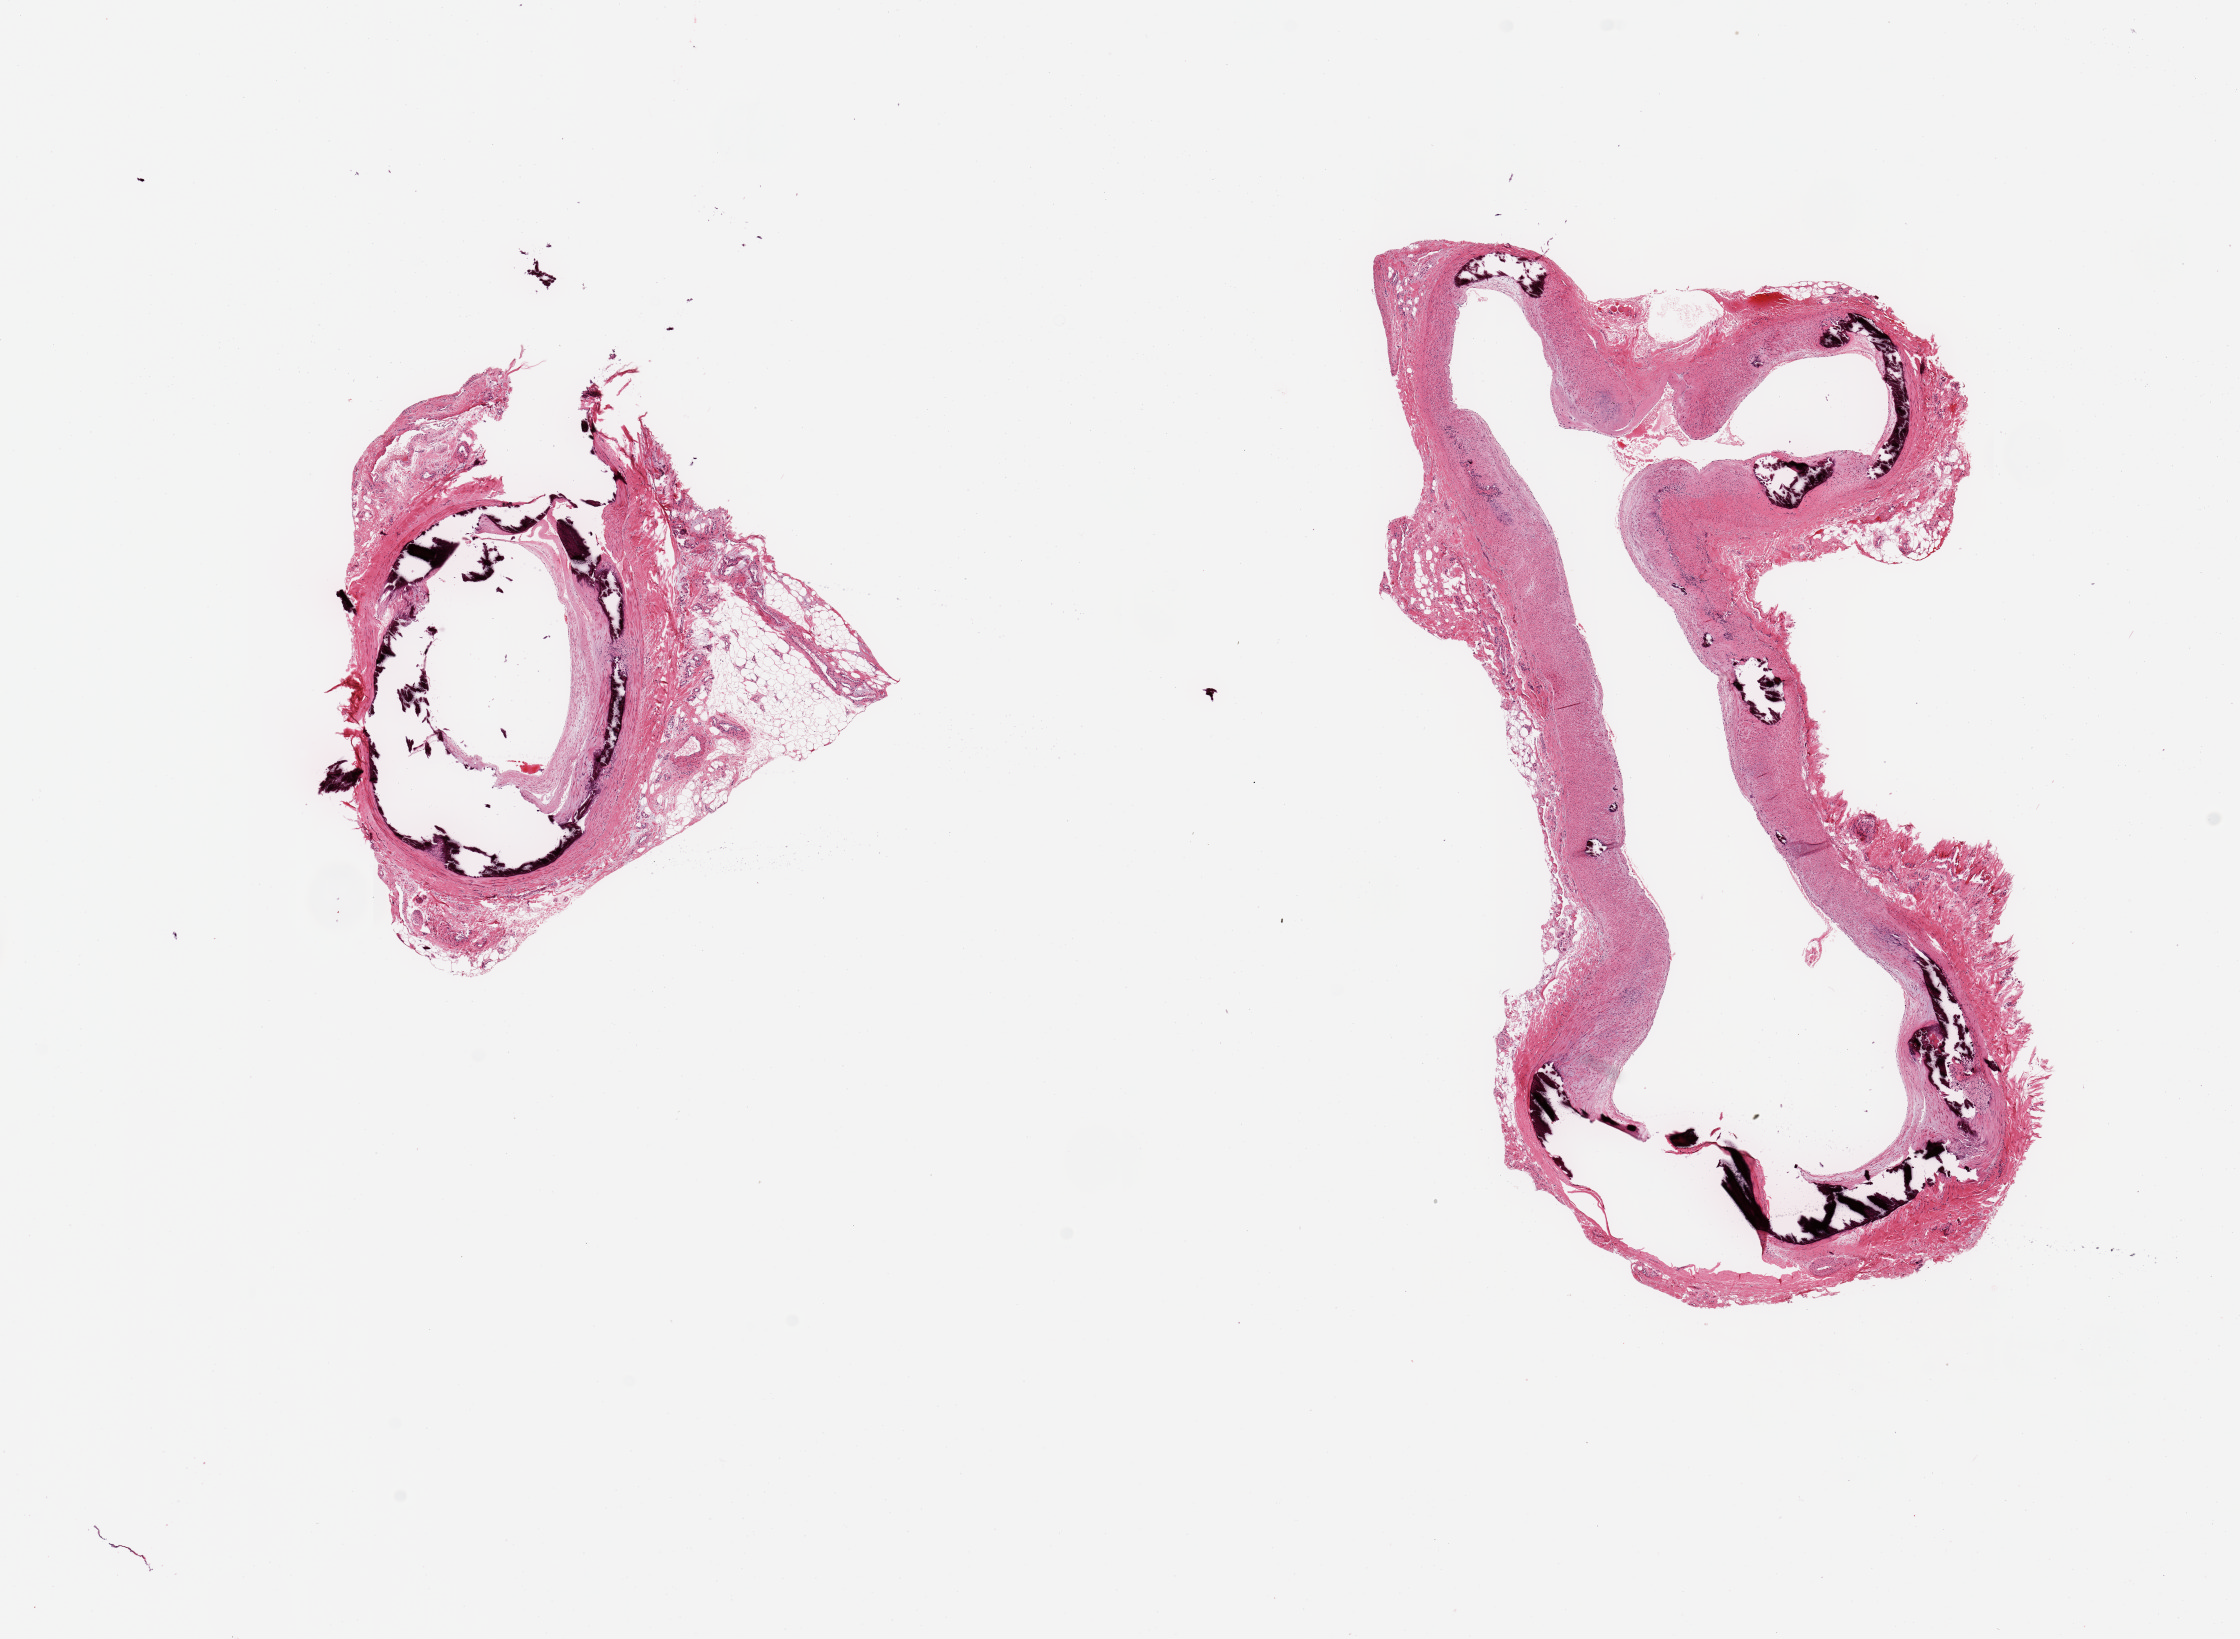
Whole-slide image, hematoxylin and eosin (H&E) stain — a low-resolution overview of the entire scanned area, about 17.7 x 13.0 mm, PAXgene-fixed paraffin-embedded (PFPE) section, sampled site (target tissue): tibial artery, tissue donor sample. Male donor.
Review note (as recorded): 2 pieces; cross section and oblique/longitudinal section of vessel with atheromatous plaque and medial calcifications; attached adventitia and fat up to ~ 1.8mm and ~0.8mm.